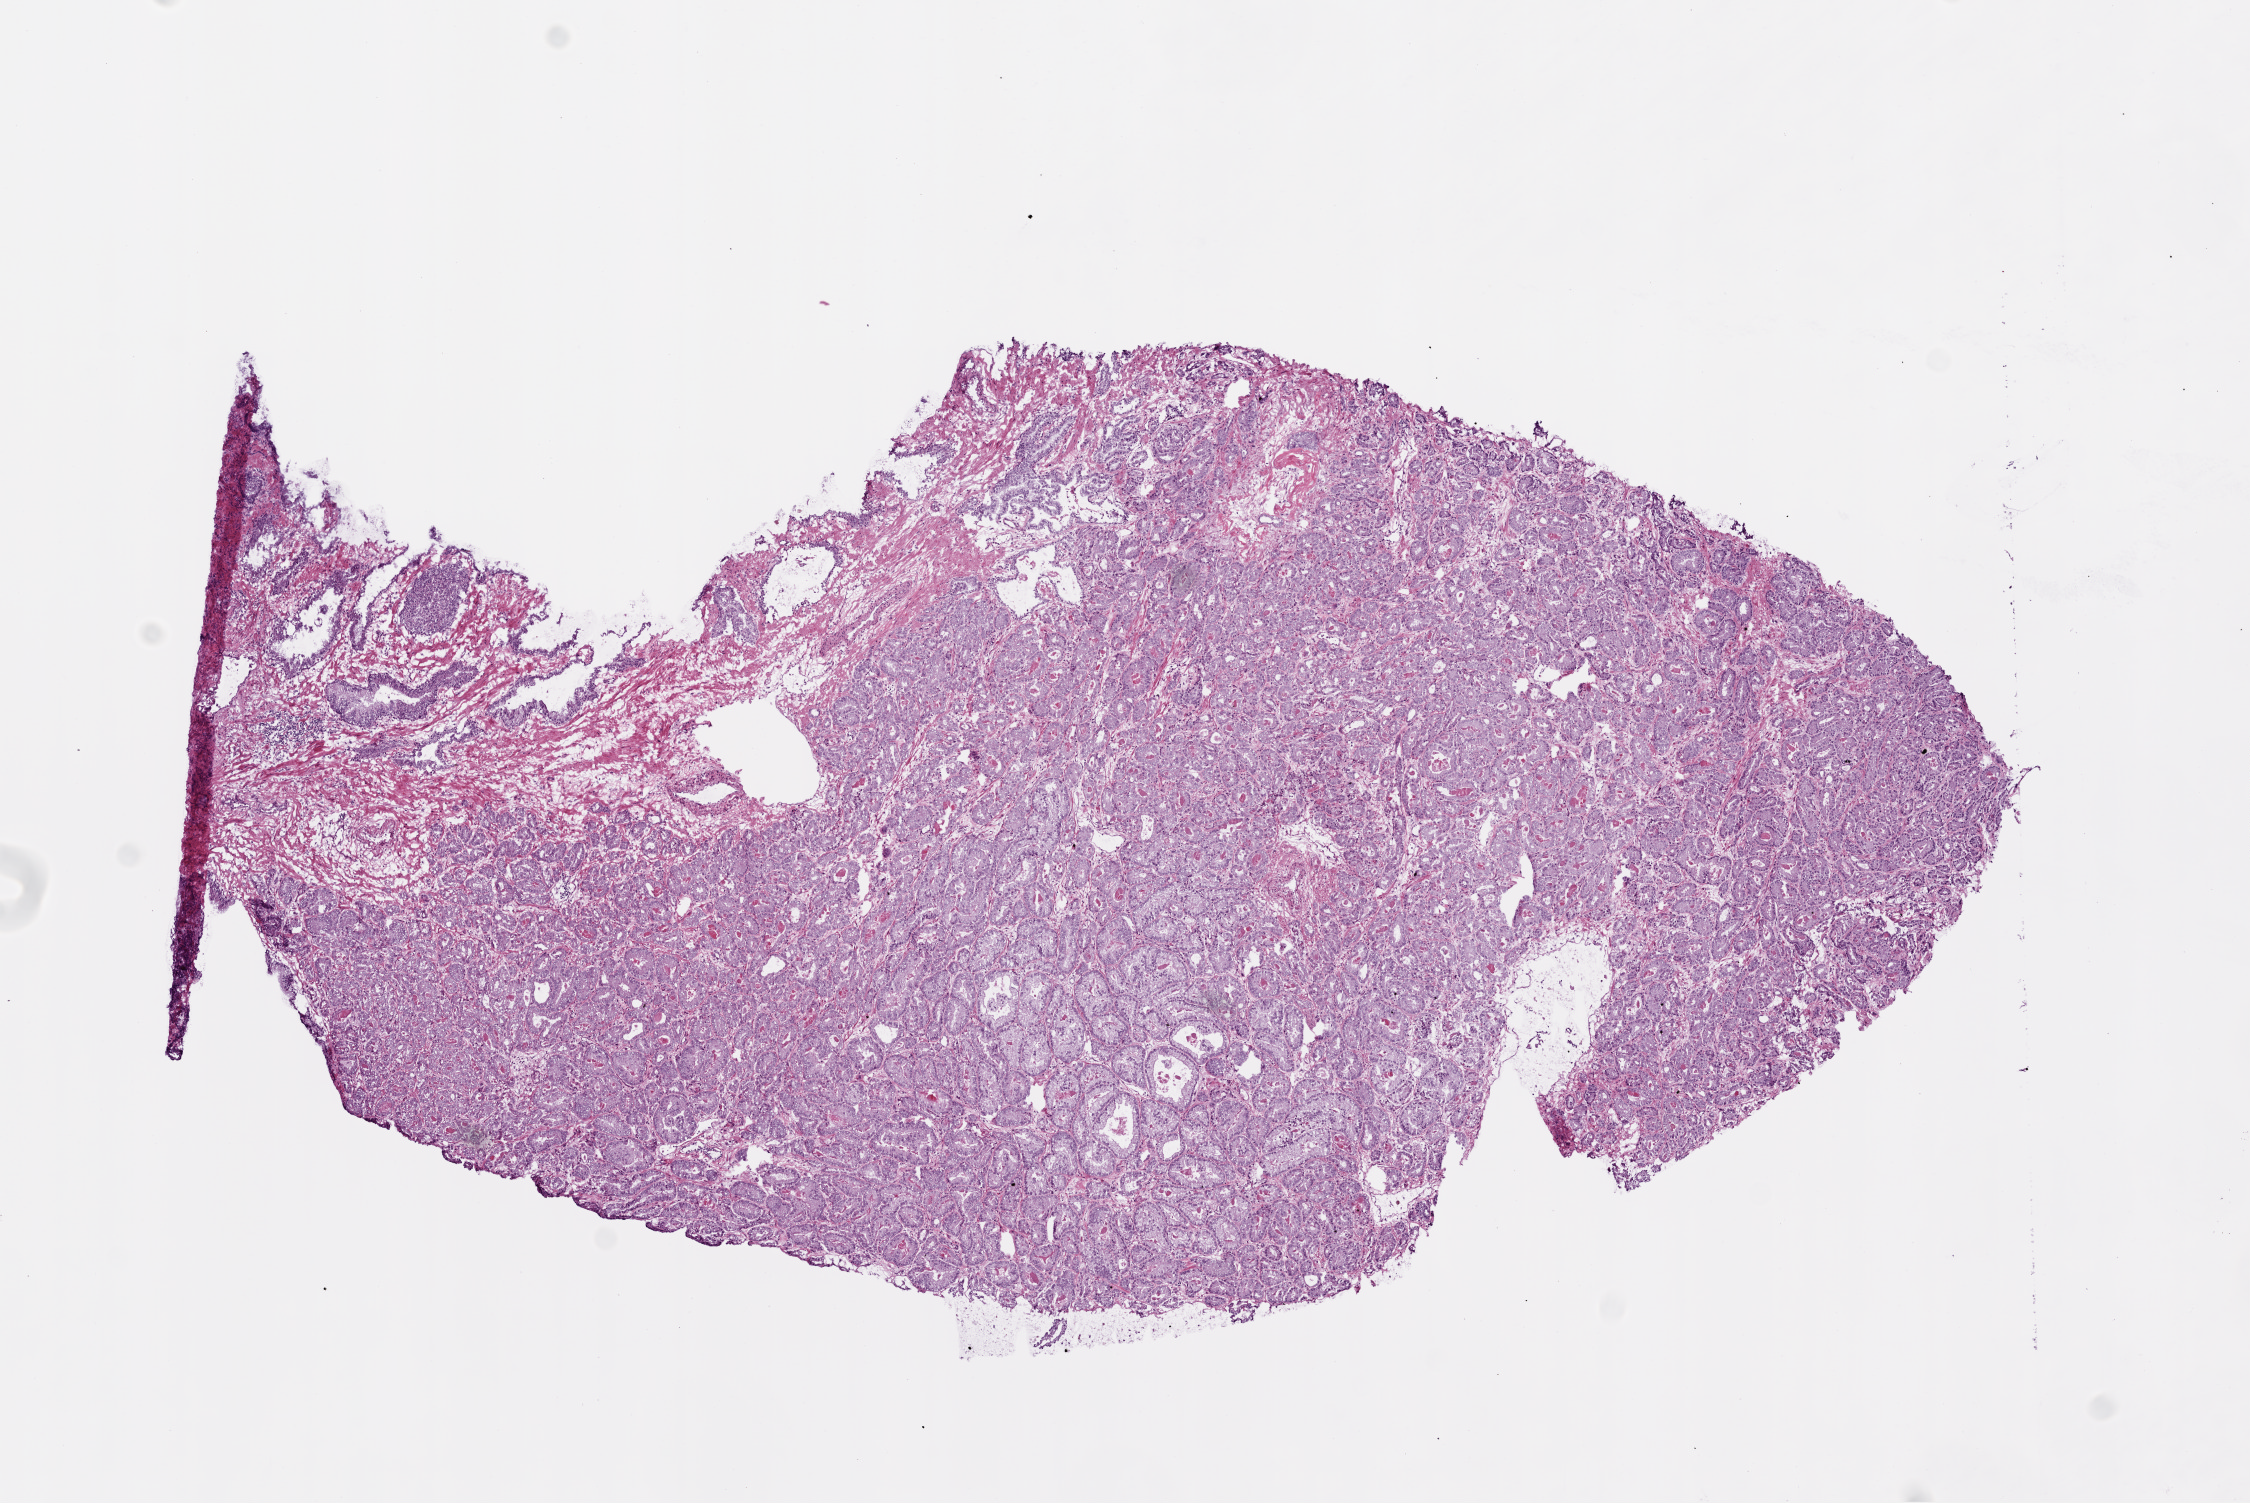
Hematoxylin and eosin (H&E) stained whole-slide image — a low-resolution overview of the entire scanned area, about 9.0 x 6.0 mm, frozen section, prostate, primary tumour sample. Male patient; age at initial diagnosis 66 years. Gleason score: 7 (4+3). Slide review estimates, as recorded: tumour cells 80%, tumour nuclei 85%, normal cells 10%, stromal cells 10%, necrosis 0%. Inflammatory infiltration, as recorded: lymphocyte infiltration 0%, monocyte infiltration 0%, neutrophil infiltration 0%.
• laterality: bilateral
• lymph nodes positive (case pathology): 0 of 19 examined
• histologic diagnosis: Acinar cell carcinoma (prostate gland)